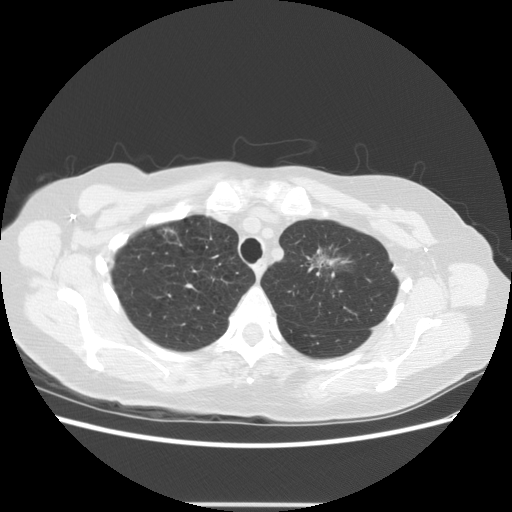
Low-dose screening chest CT, one axial slice; position 102 of 126 along the scan axis; reconstruction kernel STANDARD; 140 kVp; lung window (W 1500 / L -600 HU); 2.5 mm slice thickness; 512 × 512 image matrix.
Outlined on this slice (outlined manually by an expert reader):
- lesion 2 (tumor, upper lobe of left lung): bounding box (x1, y1, x2, y2) in pixels: (313, 253, 335, 272)